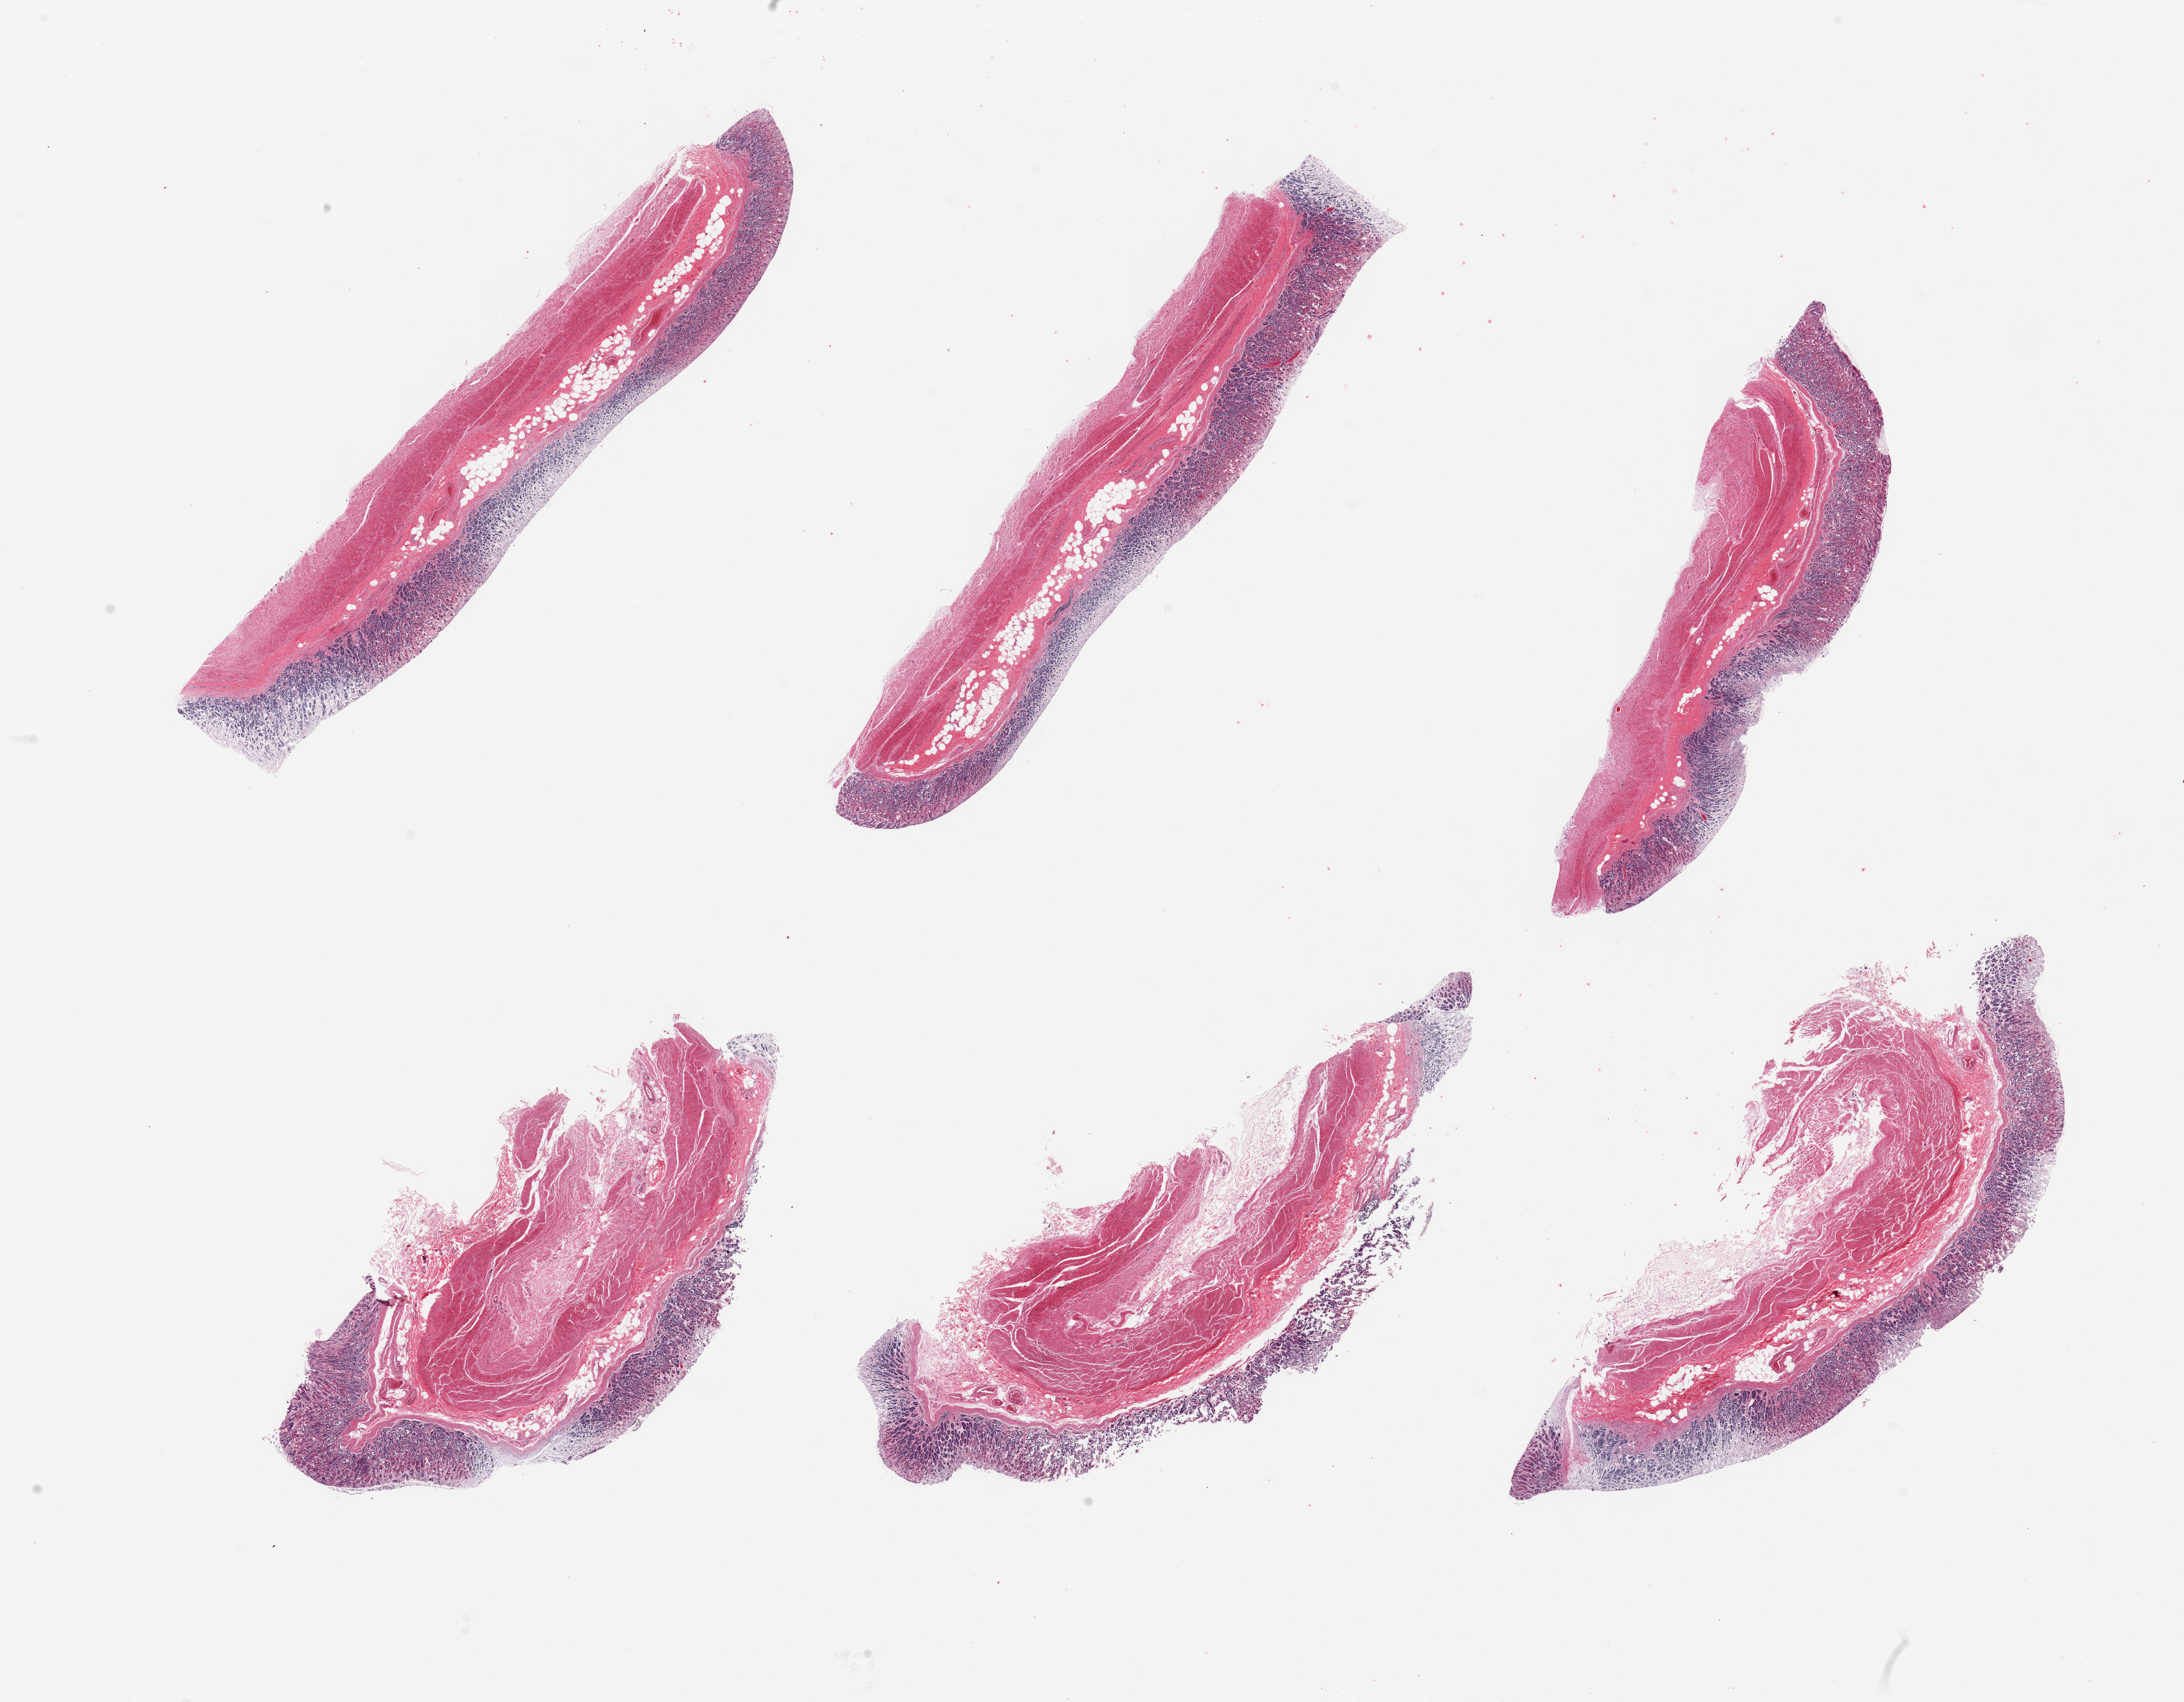
Digitized haematoxylin and eosin-stained section, brightfield, low-resolution overview of the scanned area, about 26.6 x 20.7 mm (acquisition: 20x scan); PAXgene-fixed, paraffin-embedded tissue; section of stomach (target tissue); tissue donor sample. Donor: male.
- reviewer comment on this tissue sample: 6 pieces; full thickness sections, moderate to severe mucosal autolysis